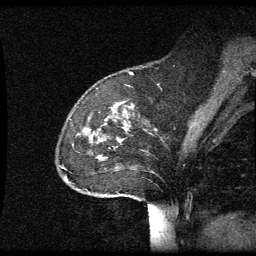
Breast MRI (dynamic contrast-enhanced), one sagittal slice; slice 18 of 60 in the series (ordered by position); dynamic contrast-enhanced series, image 2 of 3 at this slice position (ordered by acquisition); 1.5 T; TE 4.2 ms, TR 8.9 ms; 256 × 256 image matrix, field of view 200 × 200 mm. Patient: female, 49 years. Case-level facts recorded for this patient, not image findings: setting: breast cancer imaged before/during neoadjuvant chemotherapy; receptor status: HR-positive, HER2-negative.
Annotated regions visible in this slice (semi-automatic segmentation, software-assisted and operator-edited):
- analysis volume of interest (the breast-tissue region the enhancement analysis was run in; not a lesion): box from (x=64, y=102) to (x=146, y=199) px
- tumour enhancement mask (voxels above the 70 % enhancement threshold inside the analysis volume of interest): (x=120, y=140)–(x=122, y=143)